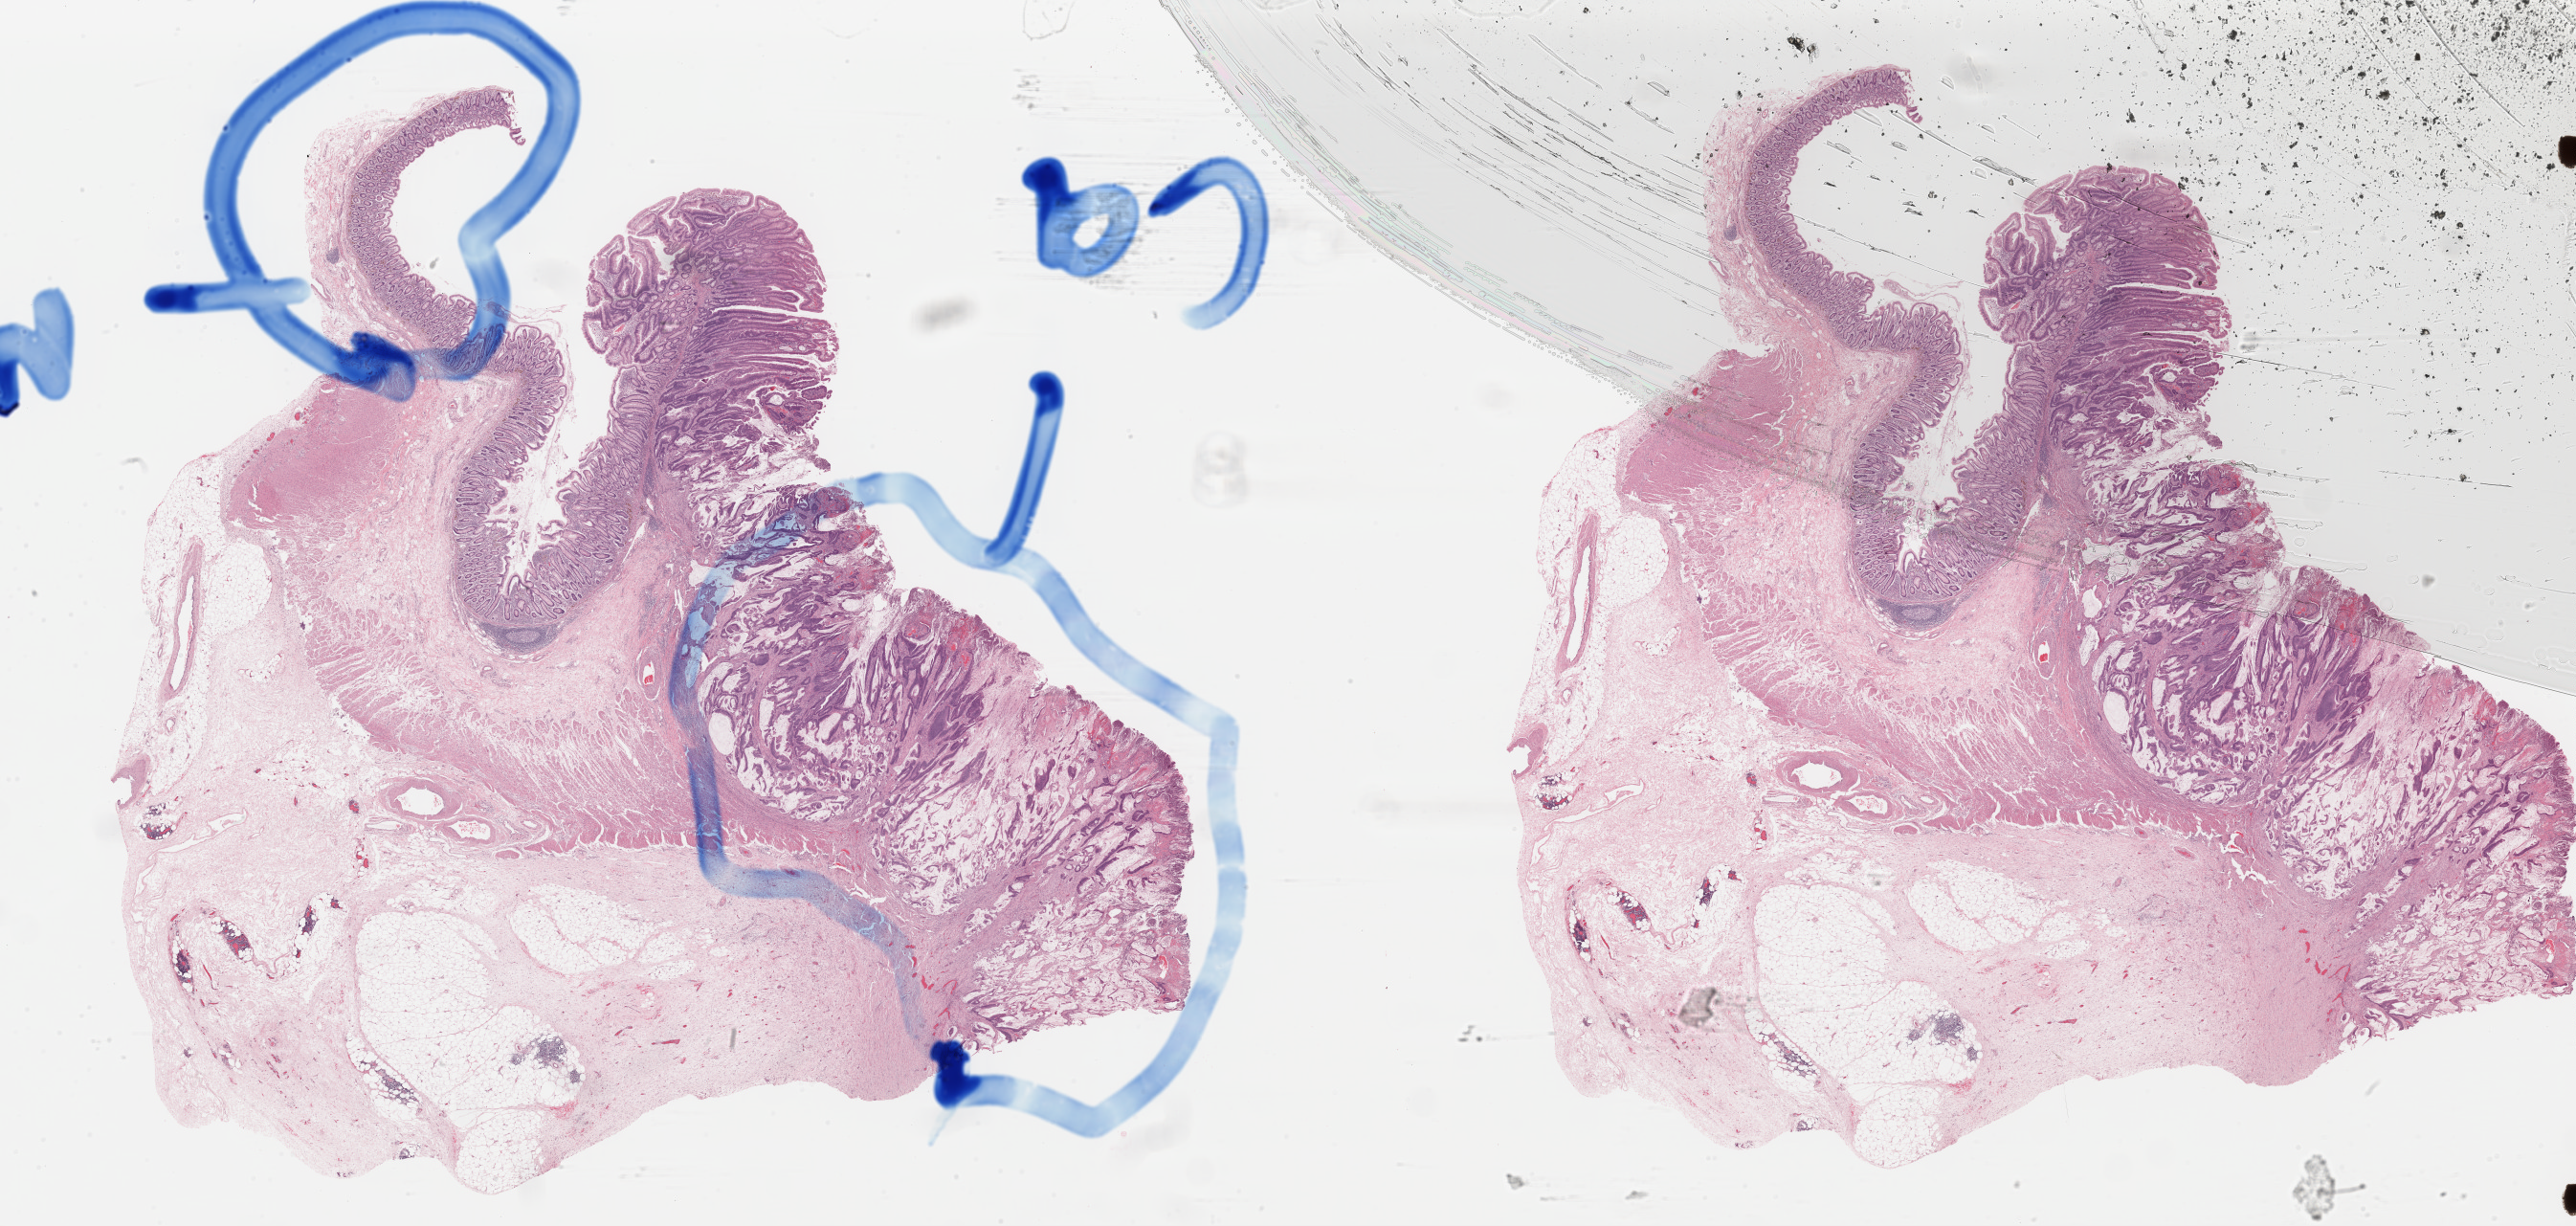
H&E-stained whole-slide image — shown as a low-resolution overview of the whole scanned area (about 42.5 x 20.2 mm). FFPE section. Sample: primary tumour, colon. Female patient; age at initial diagnosis 70 years.
- lymph nodes positive (case pathology): 0 of 10 examined
- histologic diagnosis: Mucinous adenocarcinoma (ascending colon)
- AJCC pathologic stage: IIA (6th edition)